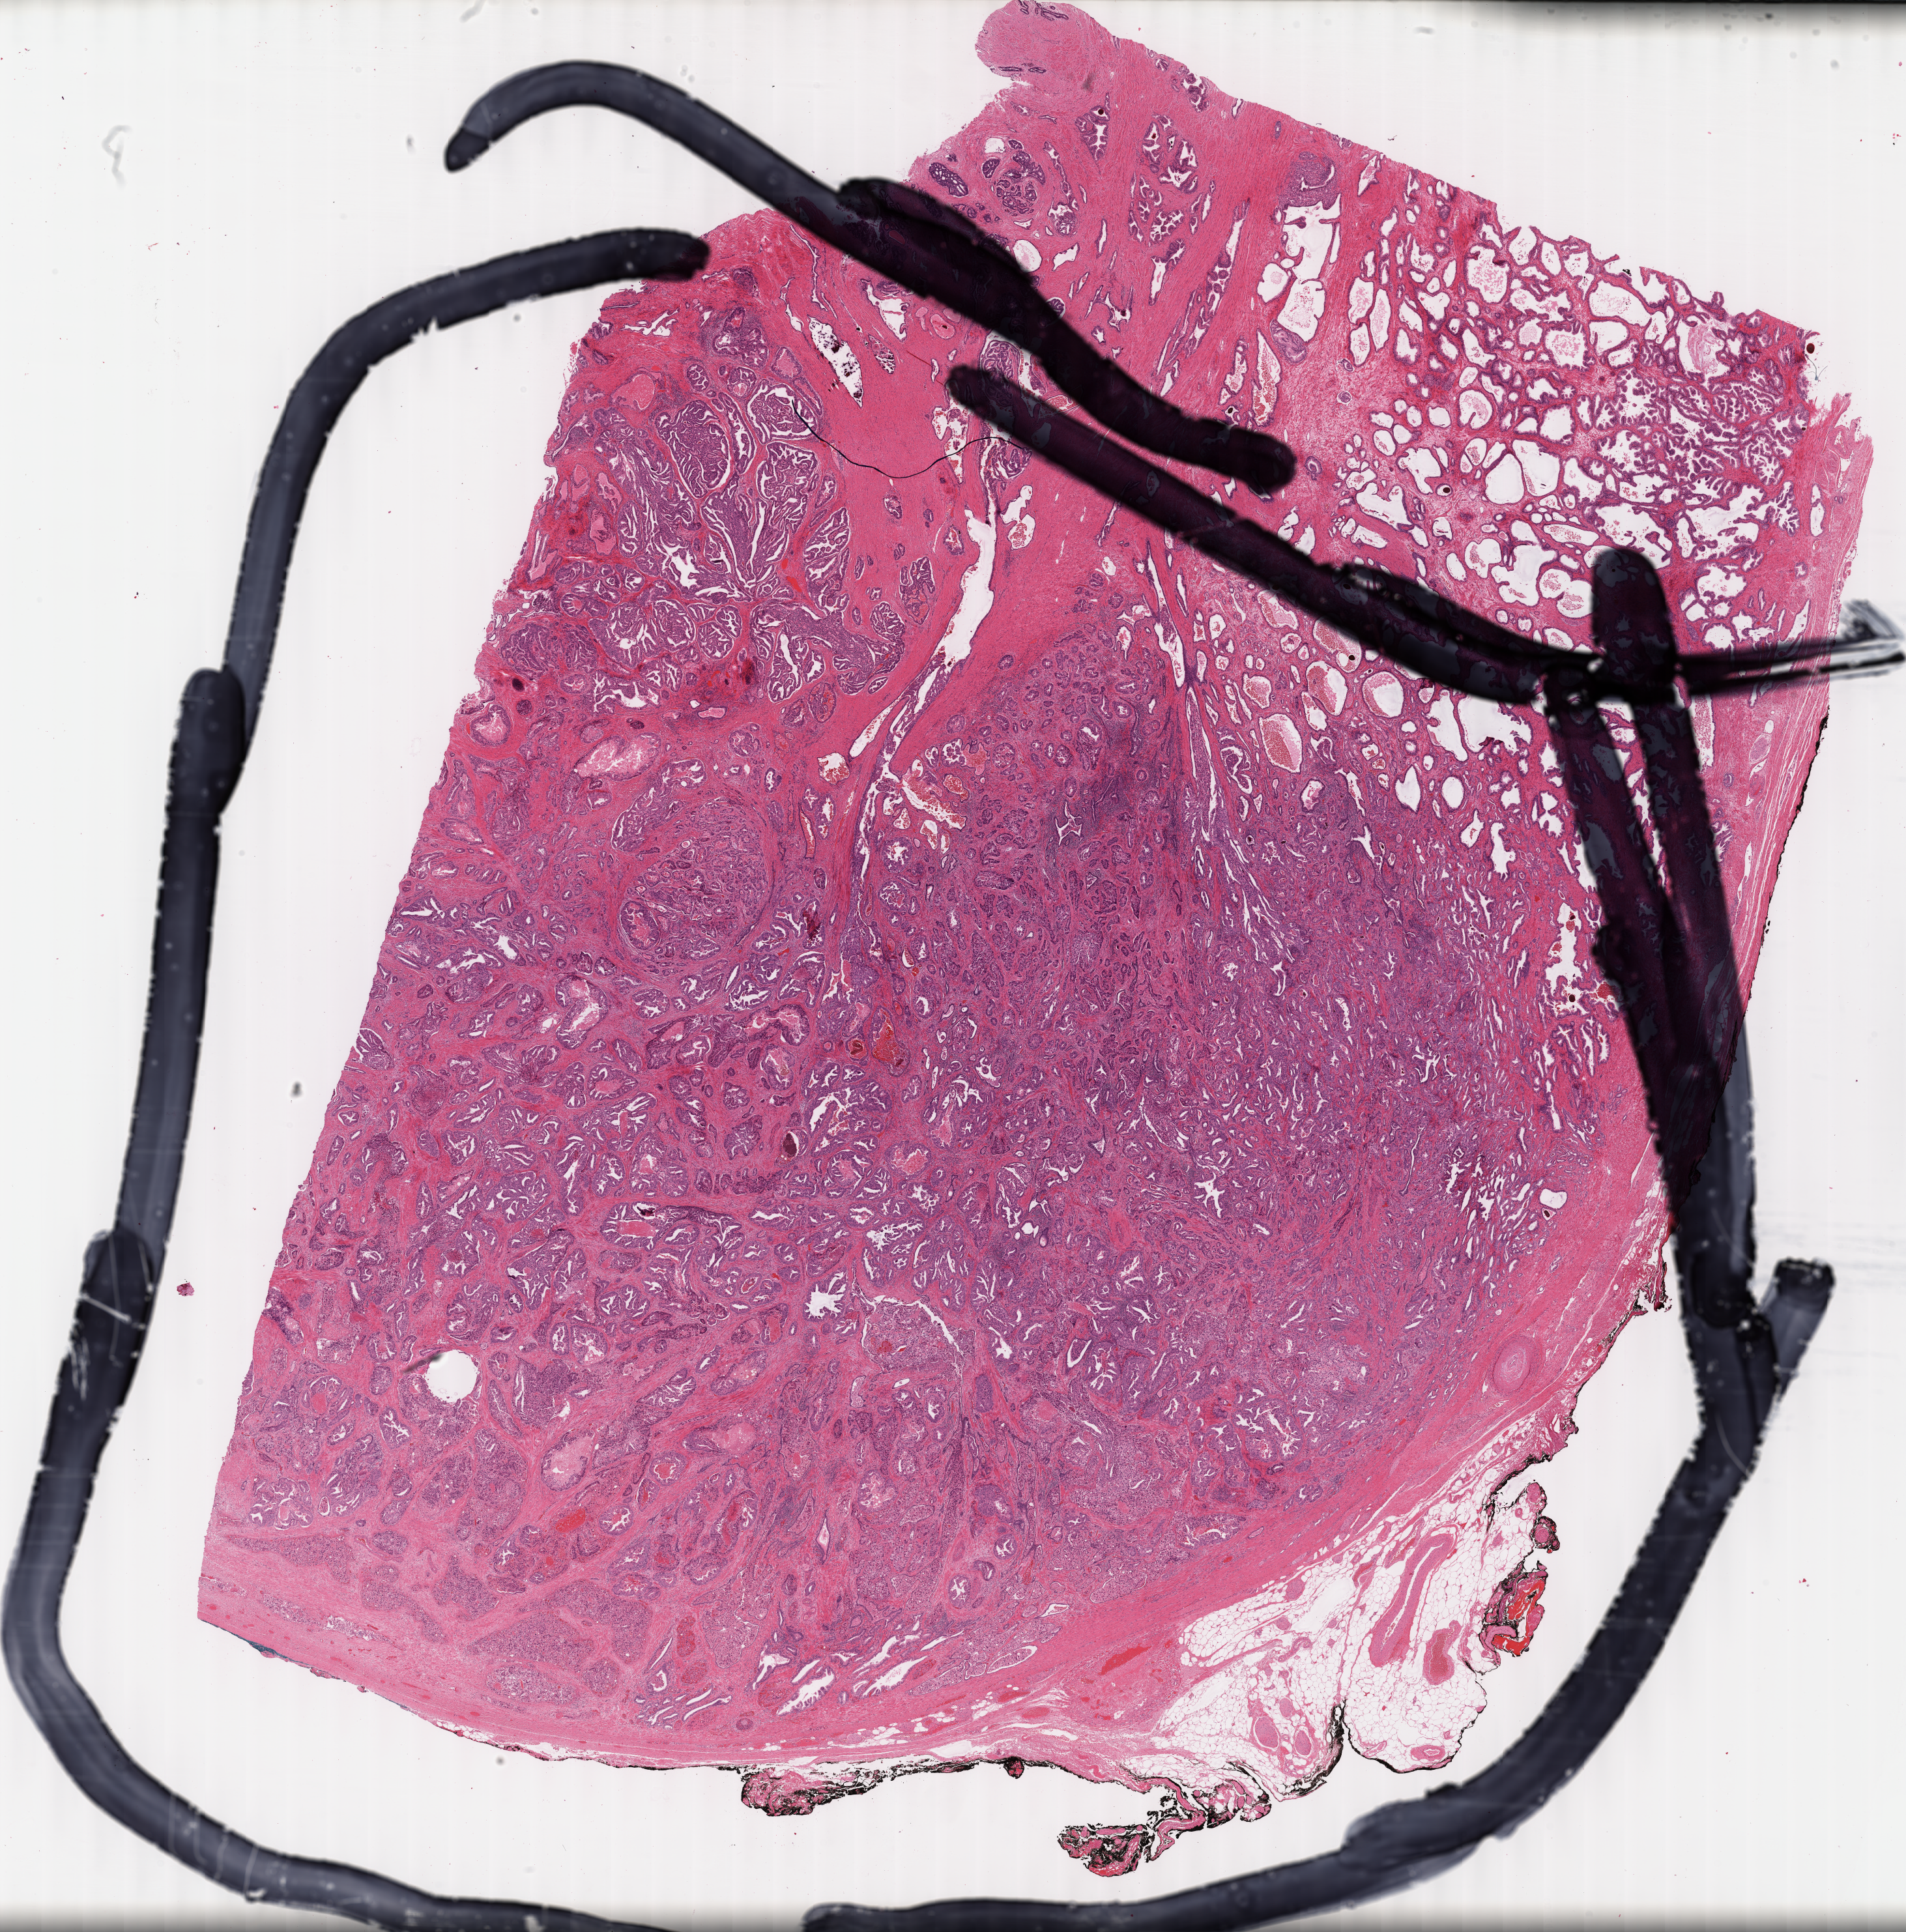
Digitized Hematoxylin and eosin (H&E) stained tissue section (whole slide) — a low-resolution overview of the entire scanned area, about 23.3 x 23.6 mm. Formalin-fixed paraffin-embedded (FFPE) diagnostic section. Primary tumour sample from the prostate. Patient: male, age at initial diagnosis 67 years.
Histologic diagnosis: Adenocarcinoma, NOS (prostate gland).